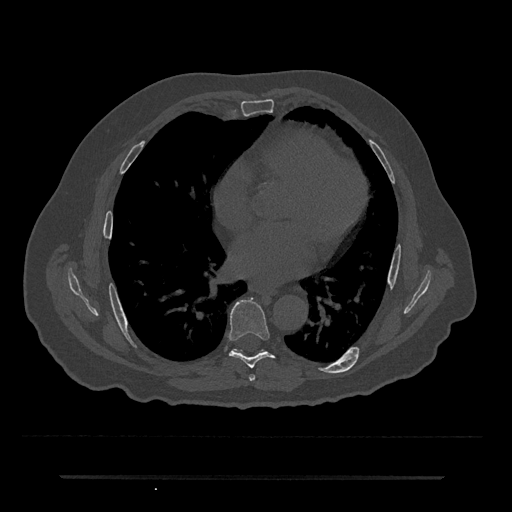
CT including the spine, one axial slice. Position 377 of 797 along the scan axis. 120 kVp. Bone window (W 1800 / L 400 HU). 0.5 mm slice thickness. 512 × 512 image matrix, field of view 437 × 437 mm. Male patient, age 69 years. From the clinical record (not read from this slice): primary cancer: prostate.
Annotated regions visible in this slice (semi-automatically segmented with operator editing):
- T6 vertebra: box from (x=249, y=374) to (x=256, y=381) px
- T7 vertebra: (x=229, y=298)–(x=275, y=368)